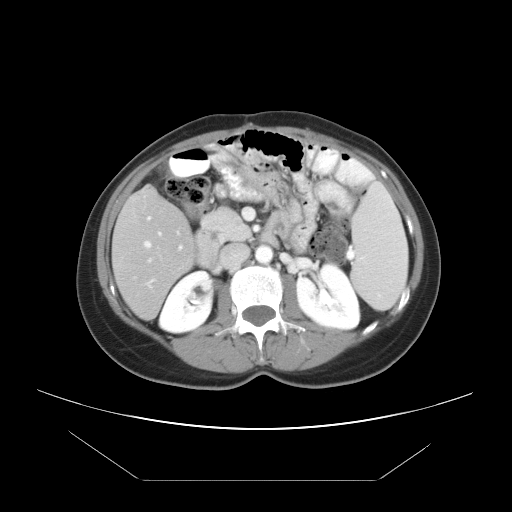
Contrast-enhanced abdominal CT, one axial slice. Position 18 of 45 along the scan axis. Reconstruction kernel STANDARD. 120 kVp. Intravenous contrast given. Soft-tissue window (W 400 / L 40 HU). 5 mm slice thickness. 512 × 512 image matrix. Female patient, age 52 years. Case-level facts recorded for this patient, not image findings: diagnosis: colorectal cancer liver metastases, imaged before liver resection; multiple liver metastases: yes; largest metastasis: 2.5 cm; disease in both lobes: no.
Annotated regions visible in this slice (expert manual segmentation):
- hepatic veins: bounding box <145,232,161,284> (left, top, right, bottom; pixels)
- liver: <114,189,194,318>
- planned liver remnant (the part of the liver to remain after resection): <114,189,192,269>
- portal vein (with intrahepatic branches): <147,216,183,263>